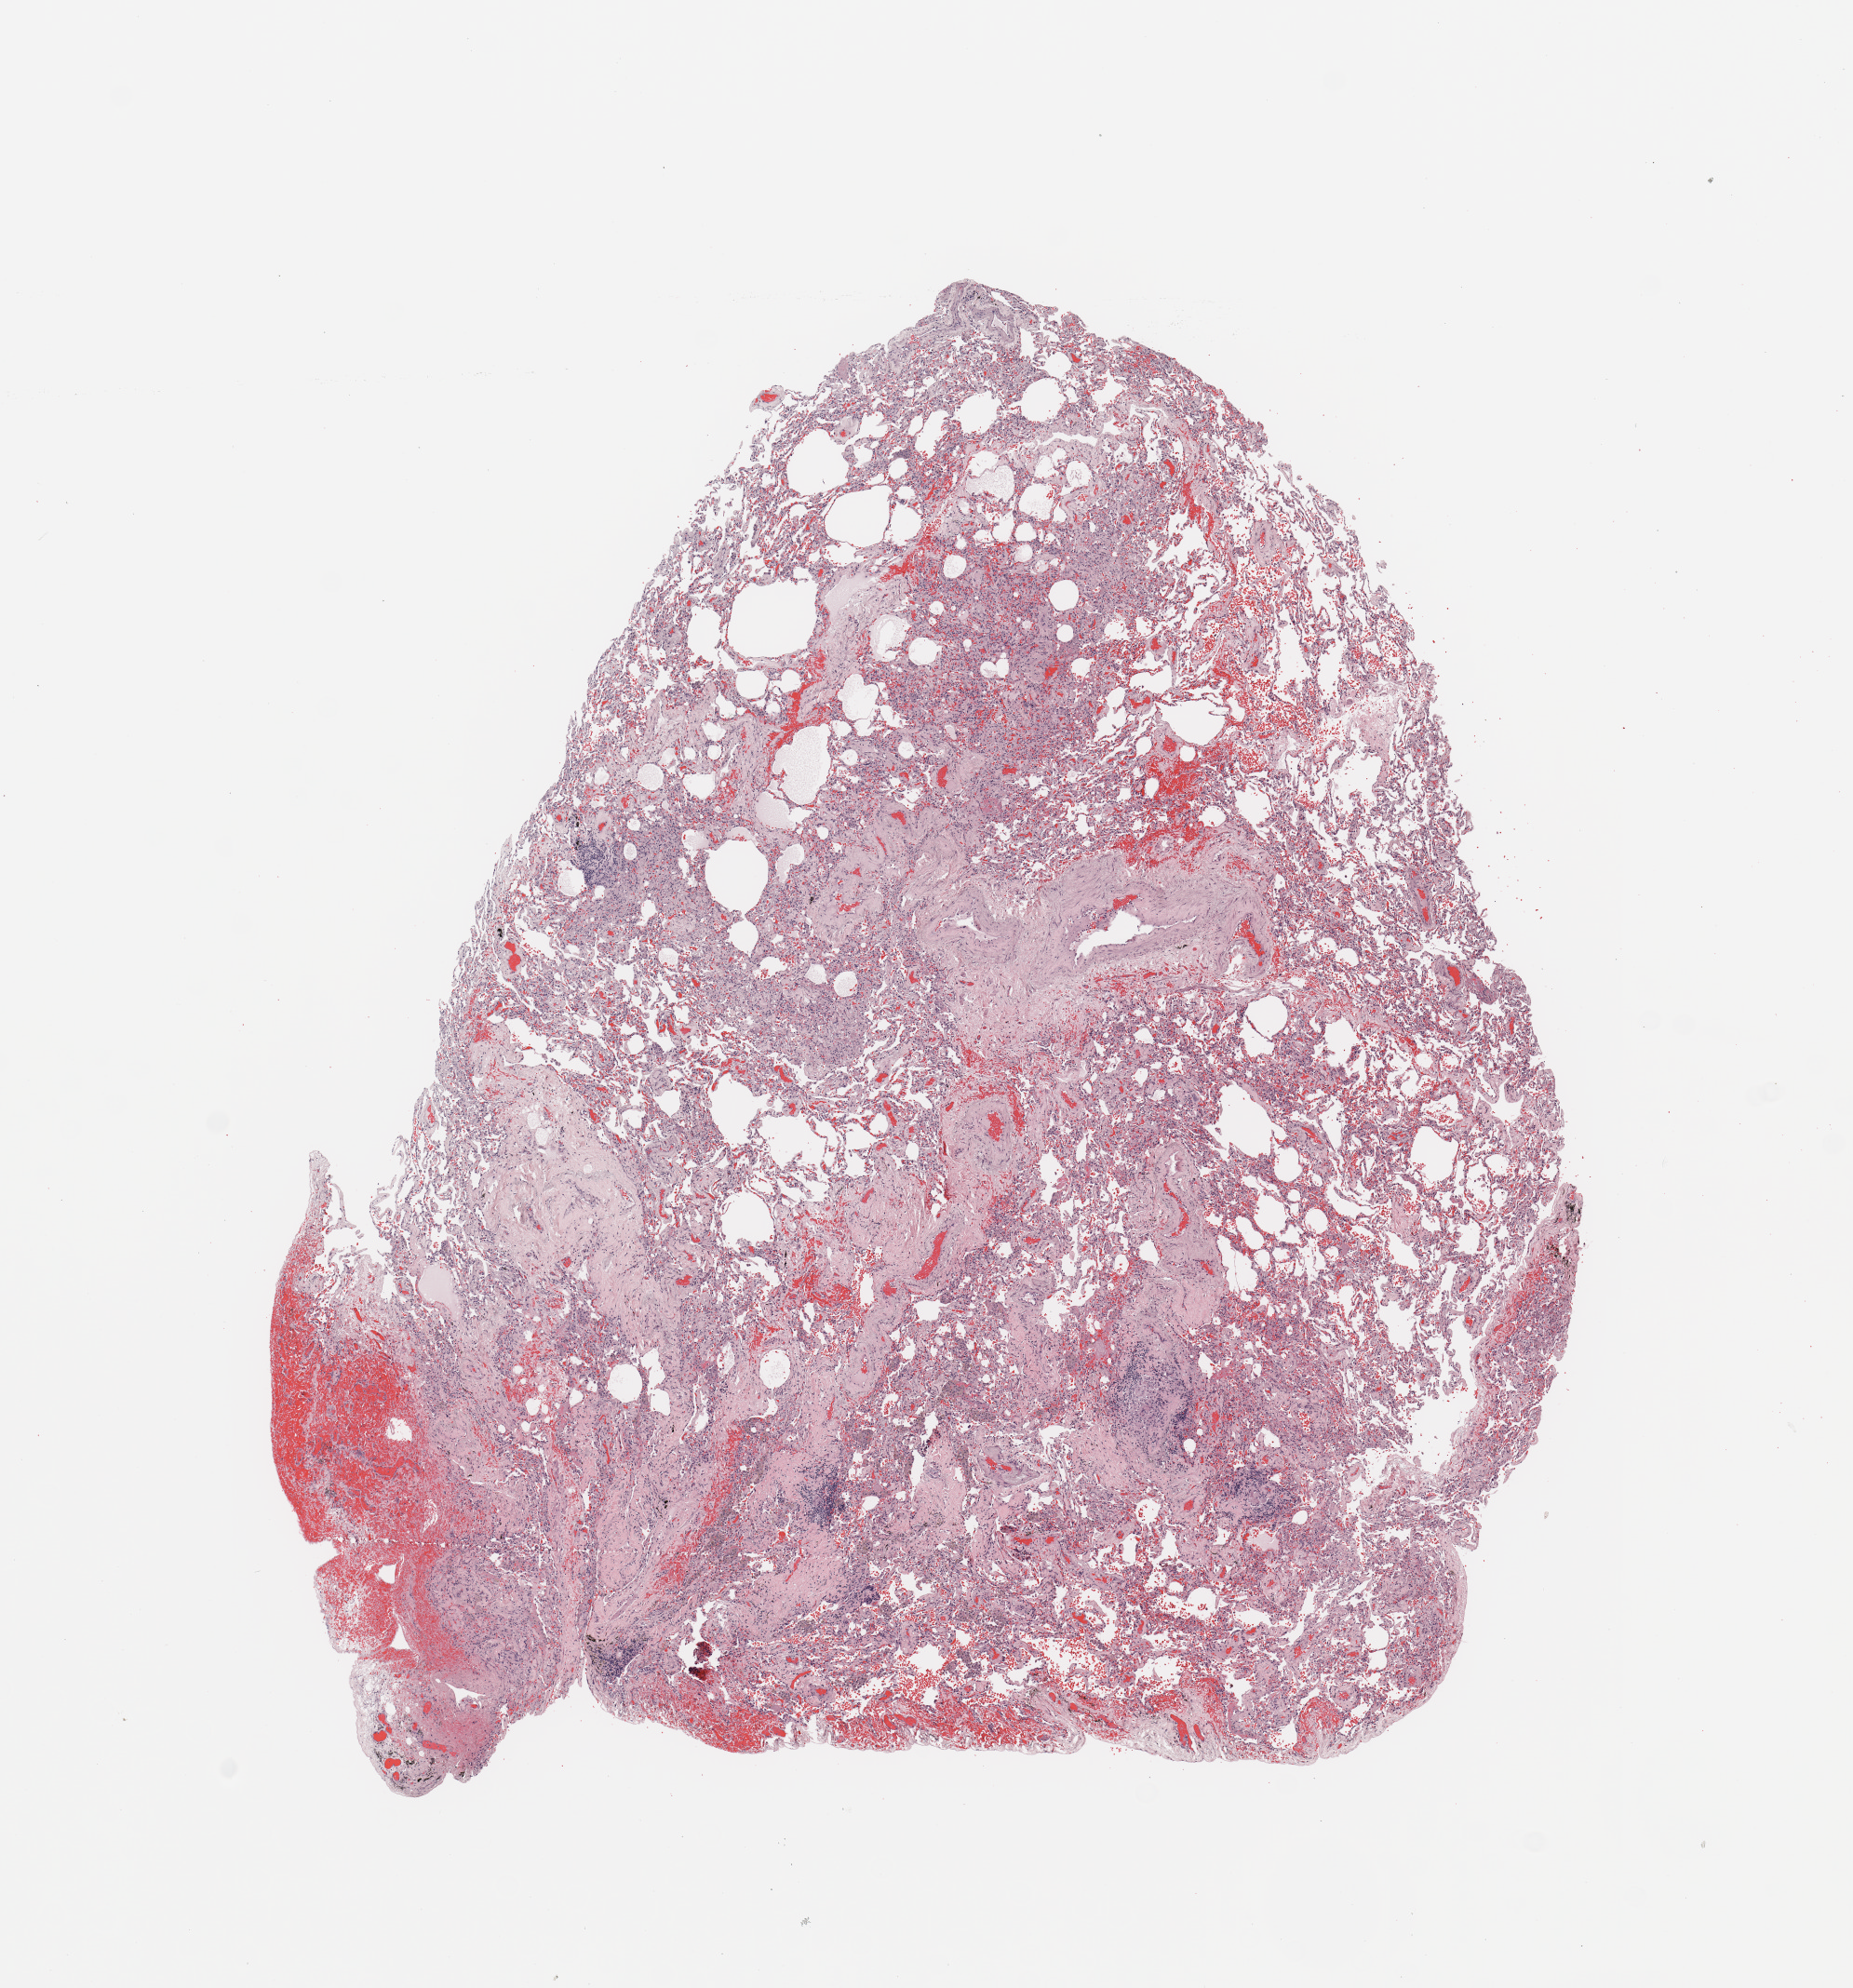
Whole-slide histology image, H&E-stained, a low-resolution overview of the entire scanned area, about 7.9 x 8.4 mm (slide scanned at 20x). Lung, normal (non-tumour) tissue. Patient: female, age 66 years.
This section: normal (non-tumour) tissue from the same patient. Patient diagnosis: Adenocarcinoma, NOS.